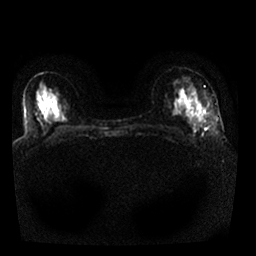
Breast MRI, one axial slice. Slice 14 of 25 in the series (ordered by position). Diffusion-weighted series; image 2 of 4 stored at this slice position (different b-values; order by instance number). 1.5 T. 4 mm slice thickness. 256 × 256 image matrix. Female patient.
Structures marked on this image (manually delineated by an expert):
- tumour on diffusion-weighted imaging: box from (x=196, y=123) to (x=201, y=130) px